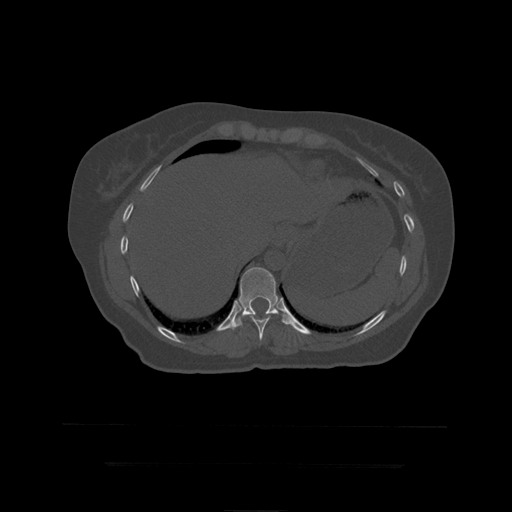
CT including the spine, one axial slice. Position 230 of 399 along the scan axis. 120 kVp. Bone window (W 1800 / L 400 HU). 1.25 mm slice thickness. 512 × 512 image matrix, field of view 450 × 450 mm. Patient age 41 years. From the clinical record (not read from this slice): primary cancer: breast.
Outlined on this slice (semi-automatically segmented with operator editing):
- T10 vertebra: box from (x=250, y=314) to (x=271, y=341) px
- T11 vertebra: (x=228, y=267)–(x=291, y=330)